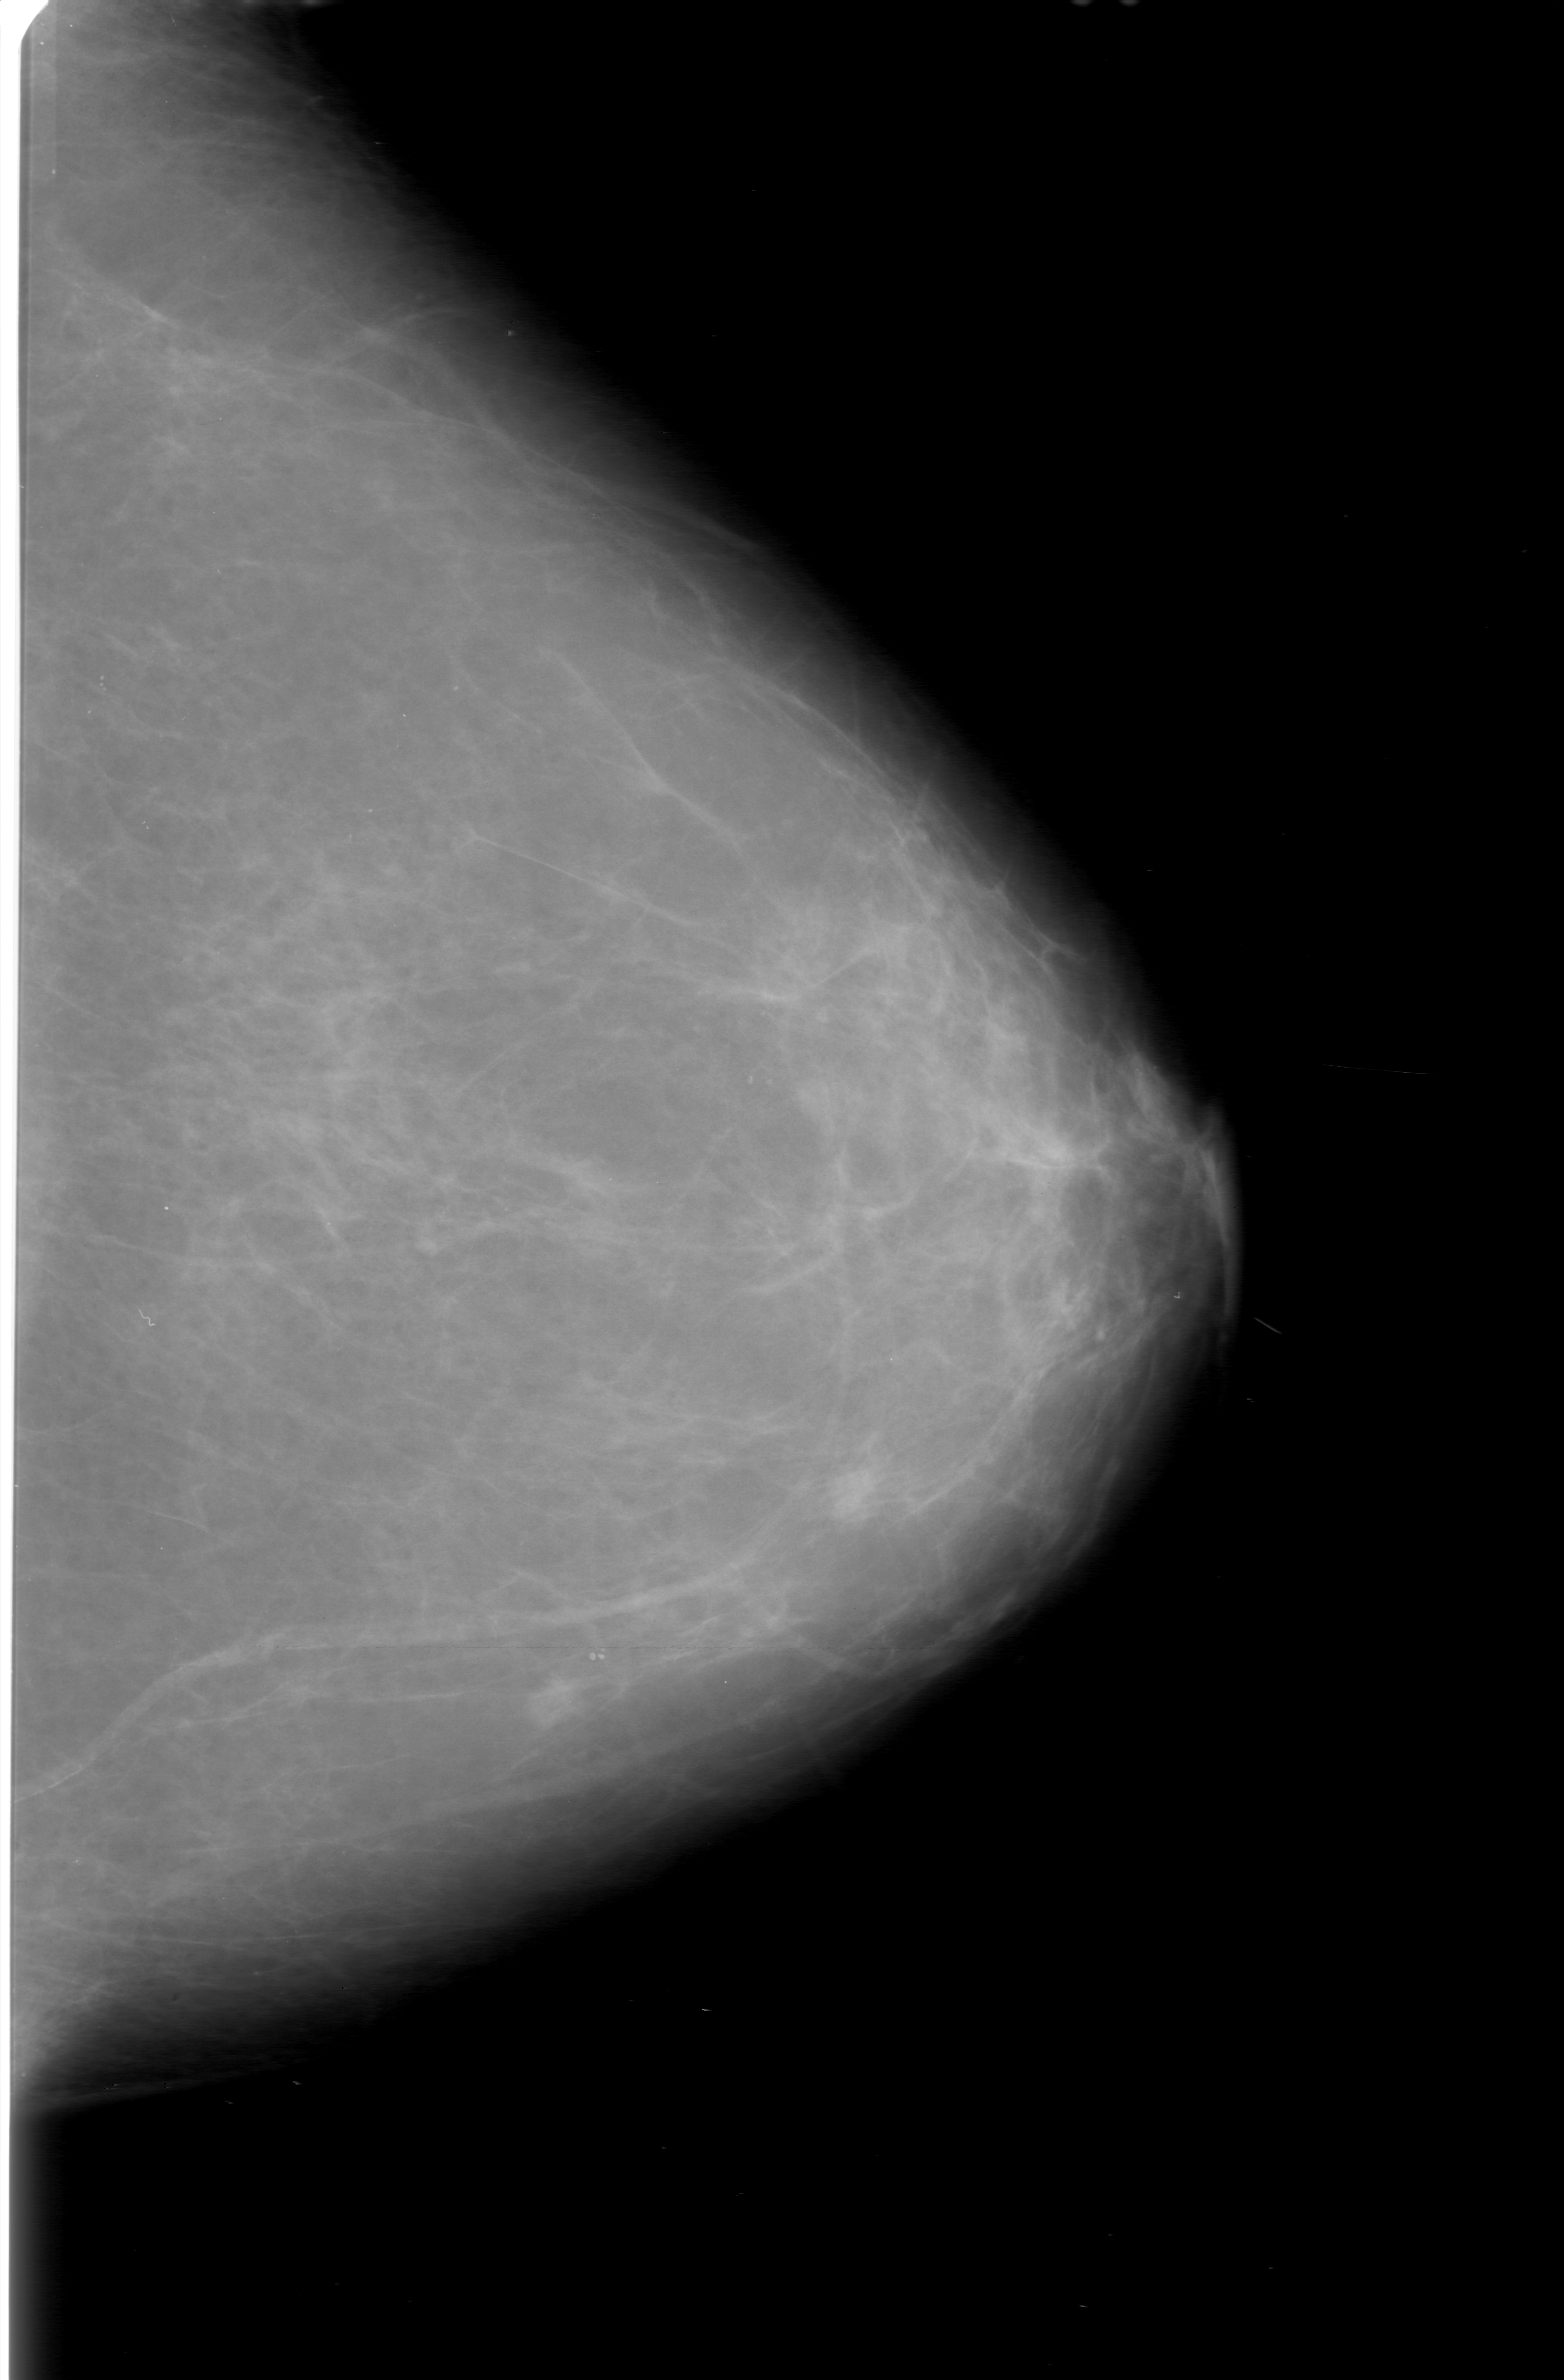
Digitized screen-film mammogram, left breast, CC view, breast composition: almost entirely fatty (BI-RADS density category 1 of 4).
- Marked findings (only marked abnormalities are described; nothing is implied about the rest of the image): mass, shape lobulated, margins obscured; BI-RADS assessment category 0 (incomplete: needs additional imaging); pathology (as recorded): malignant.